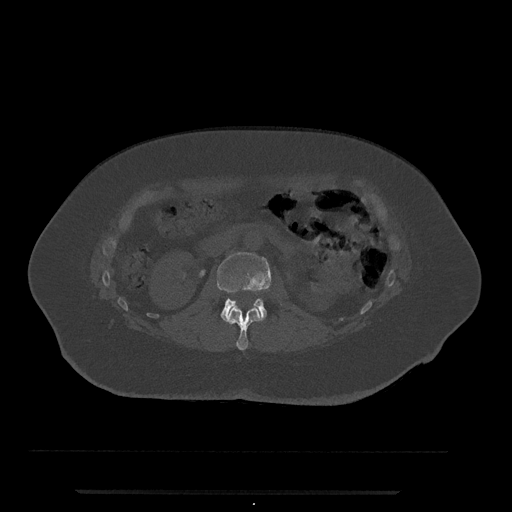
CT including the spine, one axial slice. Slice 65 of 797 in the series (ordered by position). 120 kVp. Bone window (W 1800 / L 400 HU). 0.5 mm slice thickness. 512 × 512 image matrix, field of view 440 × 440 mm. Patient: female, 51 years. Case-level facts recorded for this patient, not image findings: primary cancer: neuro.
Outlined on this slice (semi-automatic segmentation, software-assisted and operator-edited):
- L1 vertebra: bounding box (x1, y1, x2, y2) in pixels: (225, 307, 261, 351)
- L2 vertebra: (217, 252, 271, 322)